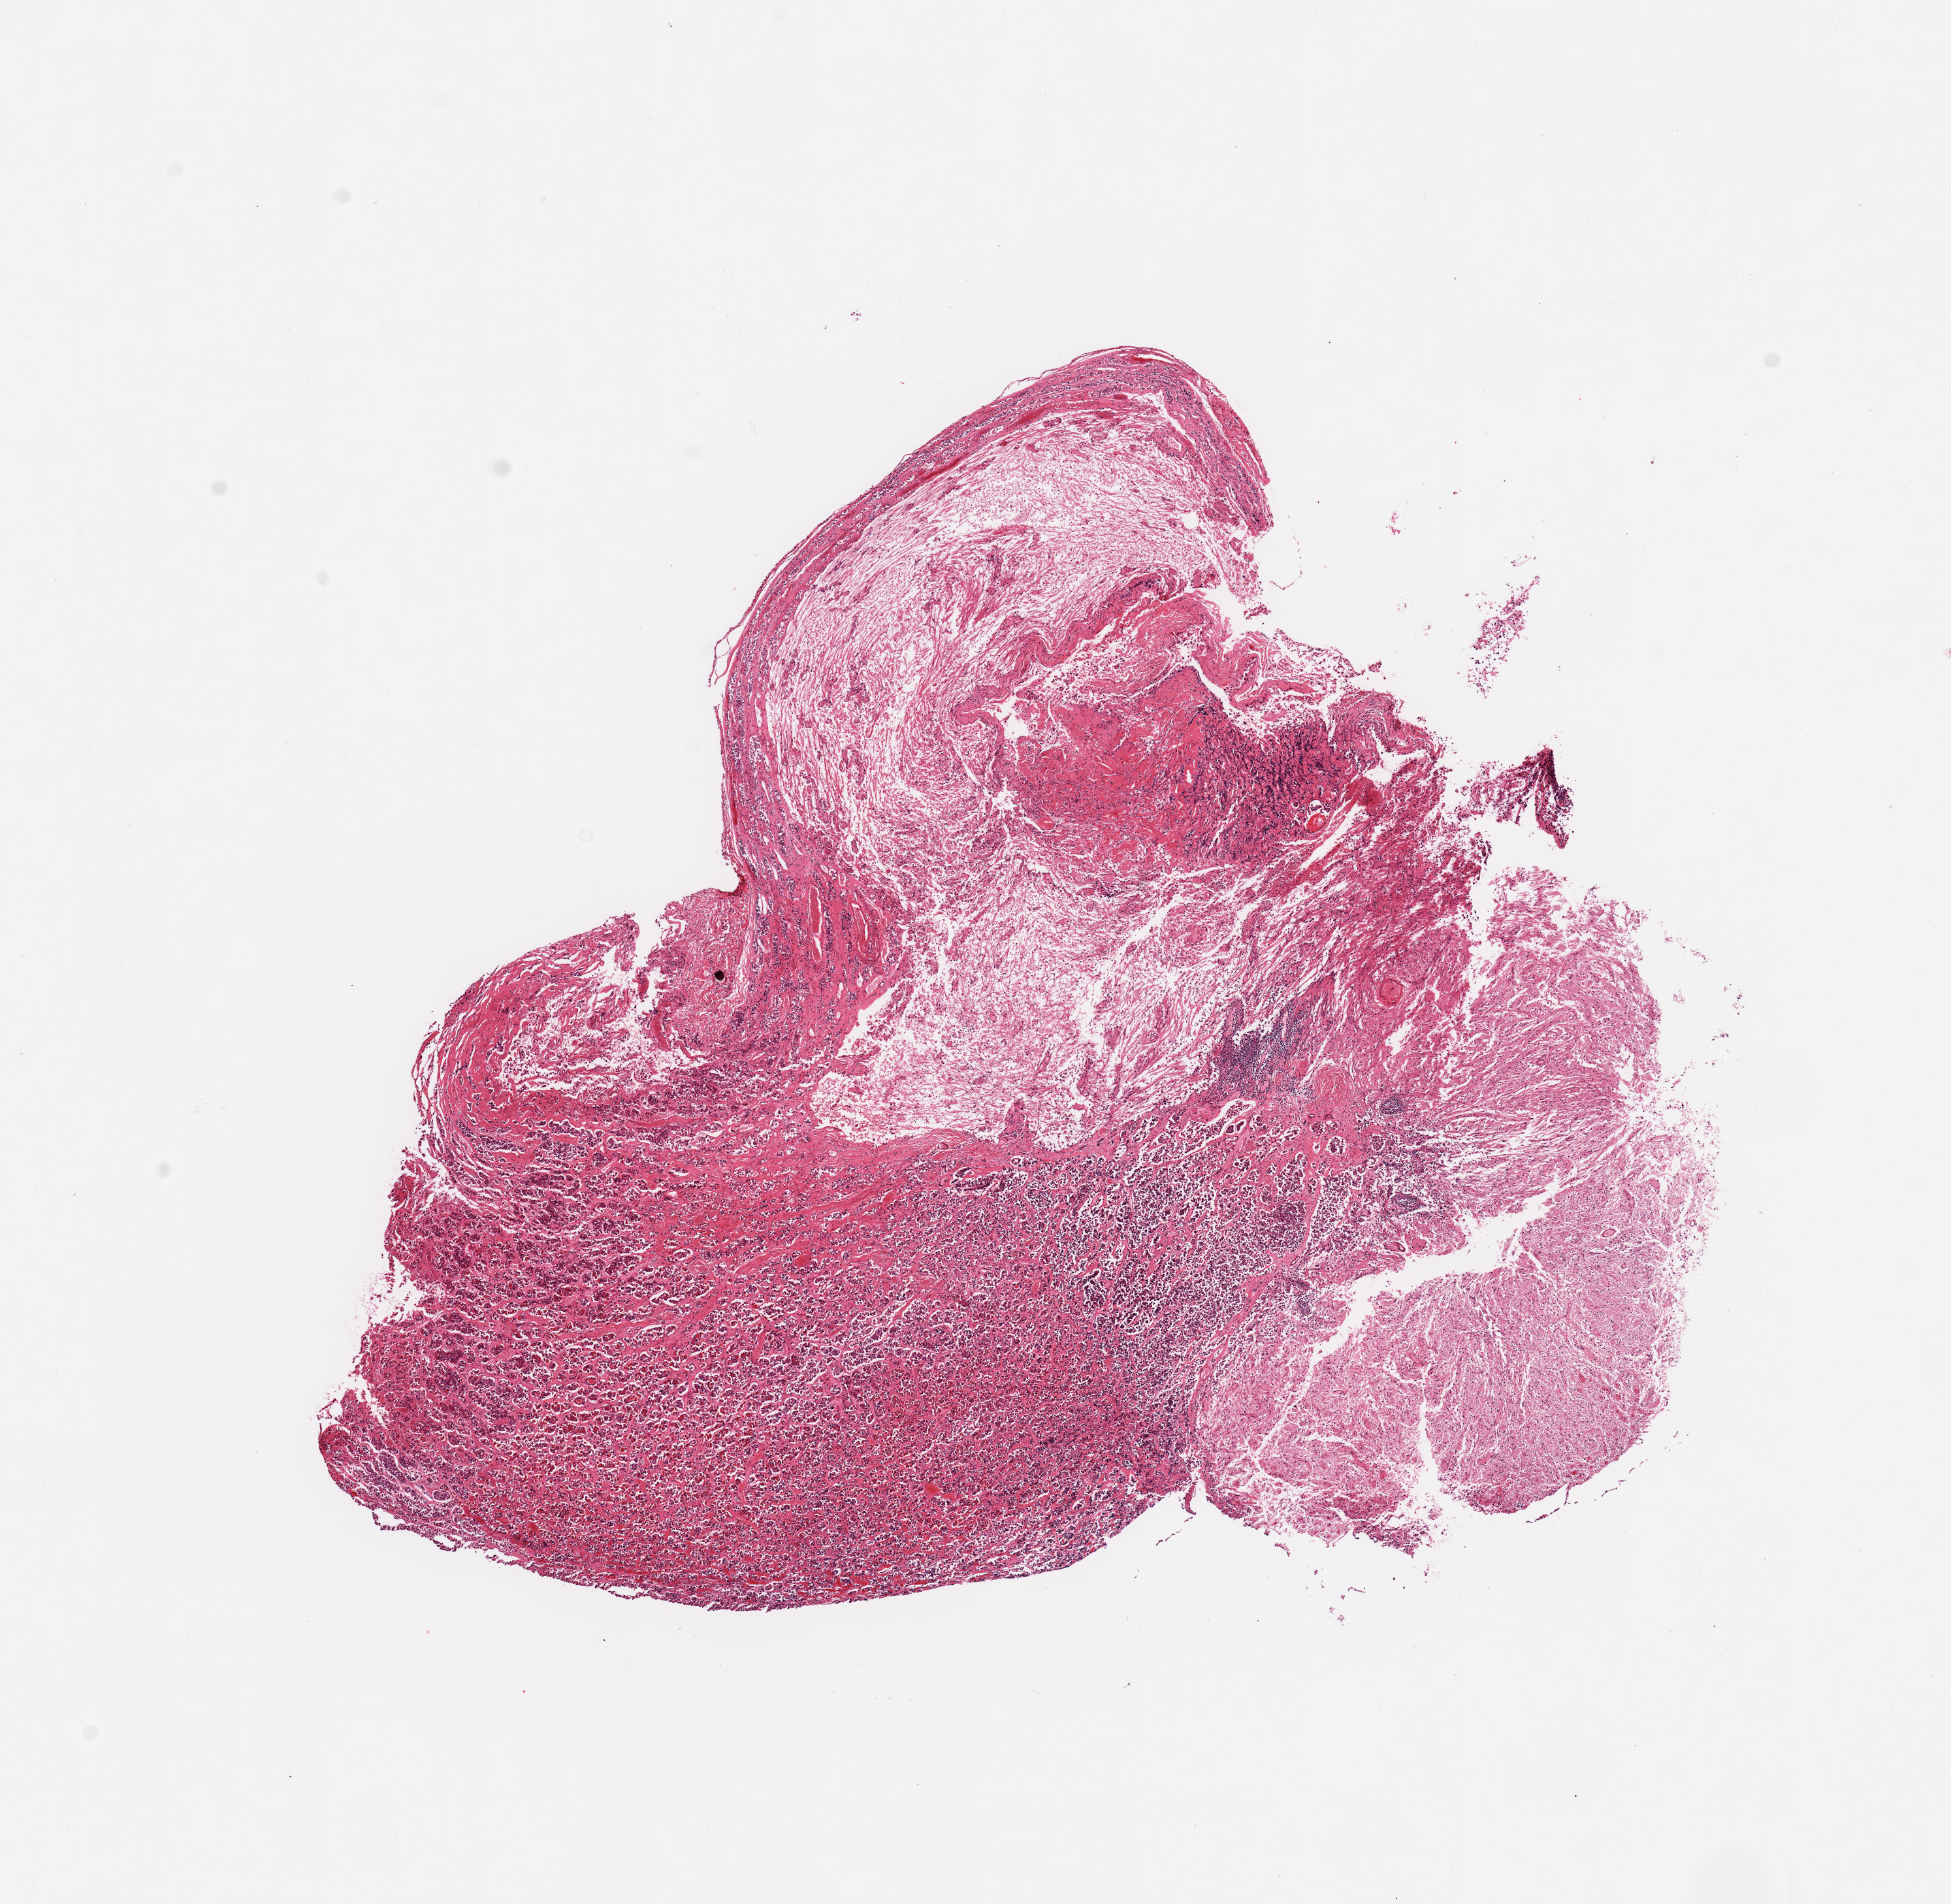
Haematoxylin and eosin whole-slide image — whole scanned area (about 11.8 x 11.5 mm) shown as a low-resolution overview, PAXgene-fixed, paraffin-embedded tissue, target tissue: pituitary, tissue donor sample. Male donor.
Pathologist's review note for this sample: 1 piece; neurohypophysis 50%.